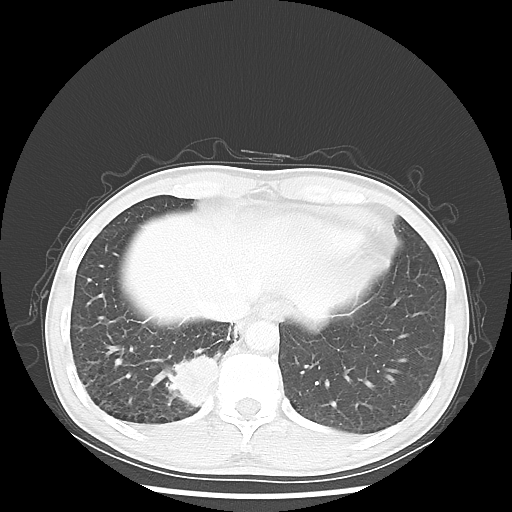
Chest CT, one axial slice. 100 kVp. Lung window (W 1500 / L -600 HU). 5 mm slice thickness. 512 × 512 image matrix, field of view 360 × 360 mm. Male patient, age 56 years. From the clinical record (not read from this slice): clinical TNM (as recorded): T2 N1 M1; histopathological grade: G1.
Structures marked on this image (bounding box drawn by a radiologist):
- lung tumour (recorded histology: adenocarcinoma): box from (x=166, y=350) to (x=222, y=412) px